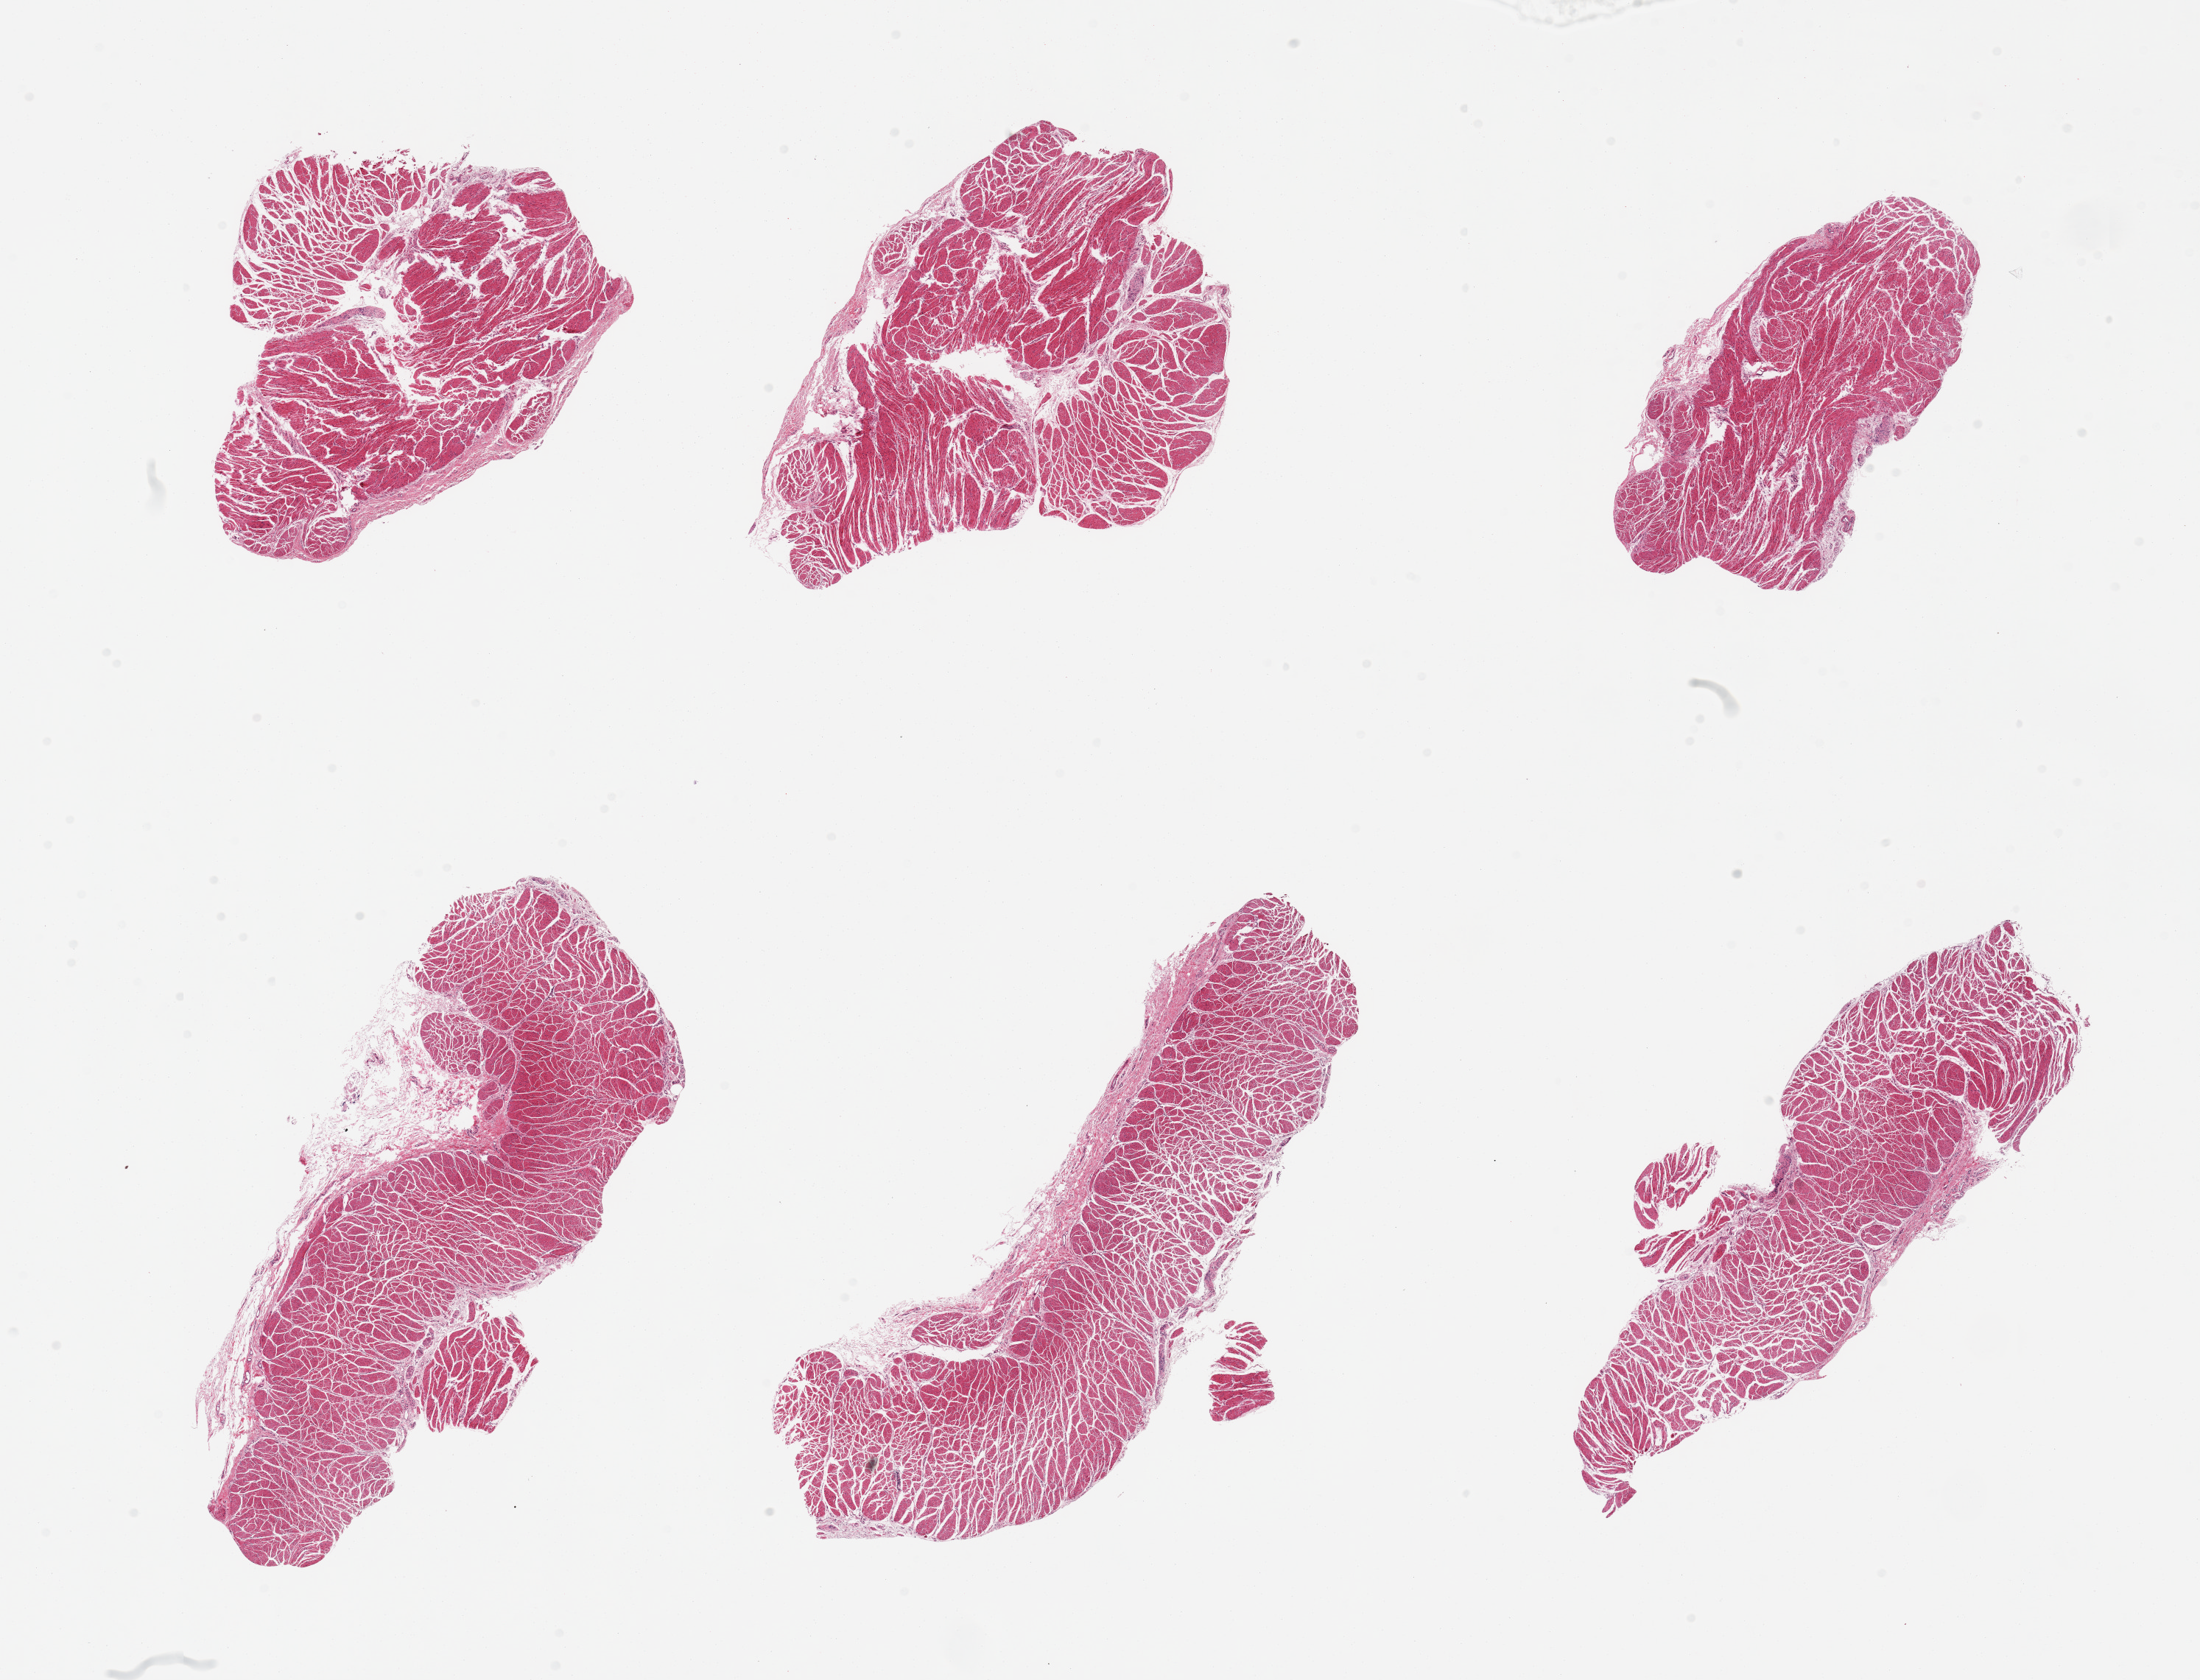
Haematoxylin and eosin whole-slide image, whole scanned area (about 23.6 x 18.0 mm) shown as a low-resolution overview. PAXgene-fixed paraffin-embedded (PFPE) section. Section of gastroesophageal junction (target tissue). Tissue donor sample. Female donor.
Reviewer comment on this tissue sample: 6 pieces.